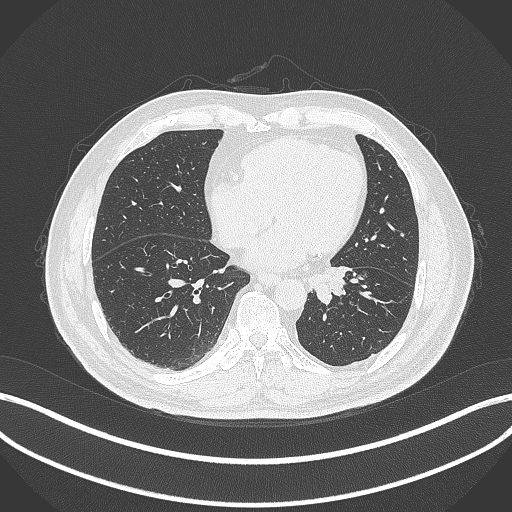
Chest CT, one axial slice. Slice 94 of 312 in the series (ordered by position). Reconstruction kernel B70f. Lung window (W 1500 / L -600 HU). 512 × 512 image matrix. Male patient, age 71 years. From the clinical record (not read from this slice): clinical TNM (as recorded): T1b N0 M0.
Annotated regions visible in this slice (rectangle marked by the reading radiologist):
- lung tumour (recorded histology: squamous cell carcinoma): box from (x=308, y=266) to (x=353, y=304) px